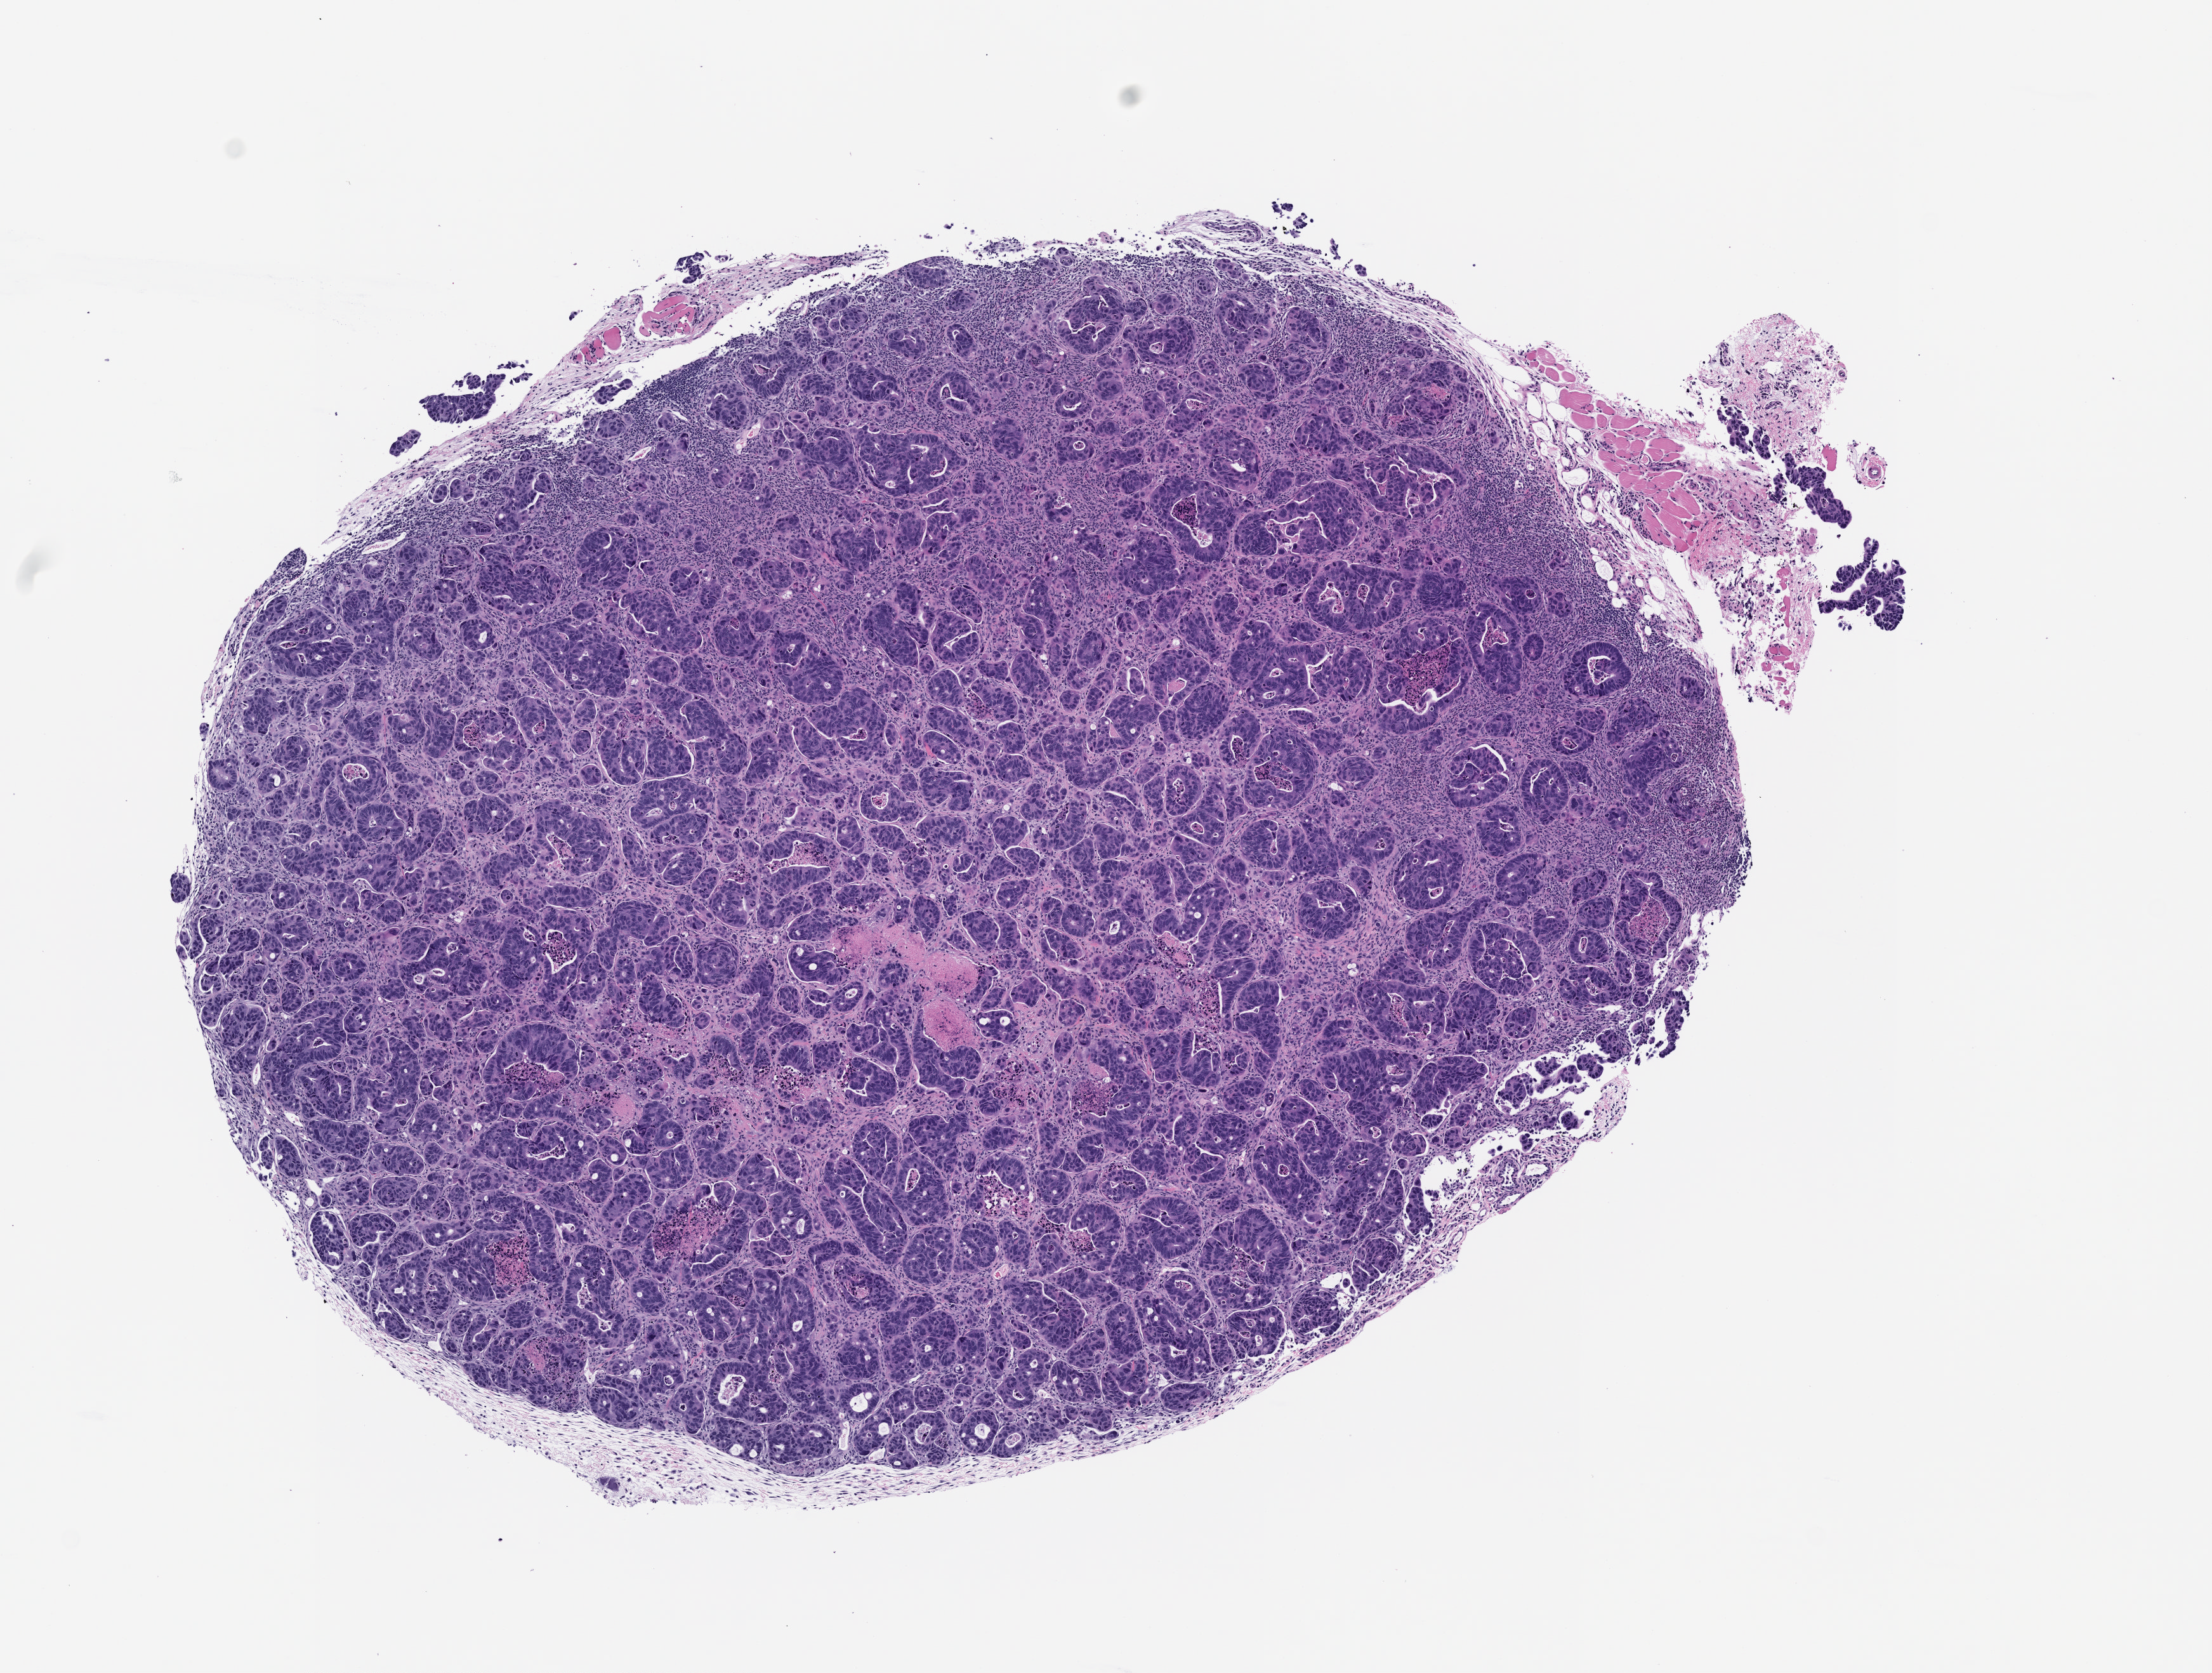
Hematoxylin and eosin (H&E) whole-slide image of a patient-derived xenograft (PDX) tumor grown in a mouse, passage 0 — low-resolution overview of the scanned area, about 7.0 x 5.3 mm; formalin-fixed paraffin-embedded section; tumor site category: rectum.
Originating patient diagnosis: Rectal Adenocarcinoma.